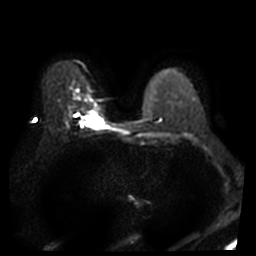
Breast MRI, one axial slice; slice 26 of 46 in the series (ordered by position); diffusion-weighted series; image 2 of 4 stored at this slice position (different b-values; order by instance number); 3 T; 5 mm slice thickness; 256 × 256 image matrix, field of view 340 × 340 mm. Female patient.
Annotated regions visible in this slice (outlined manually by an expert reader):
- tumour on diffusion-weighted imaging: bounding box [x1, y1, x2, y2] px = [87, 115, 103, 126]